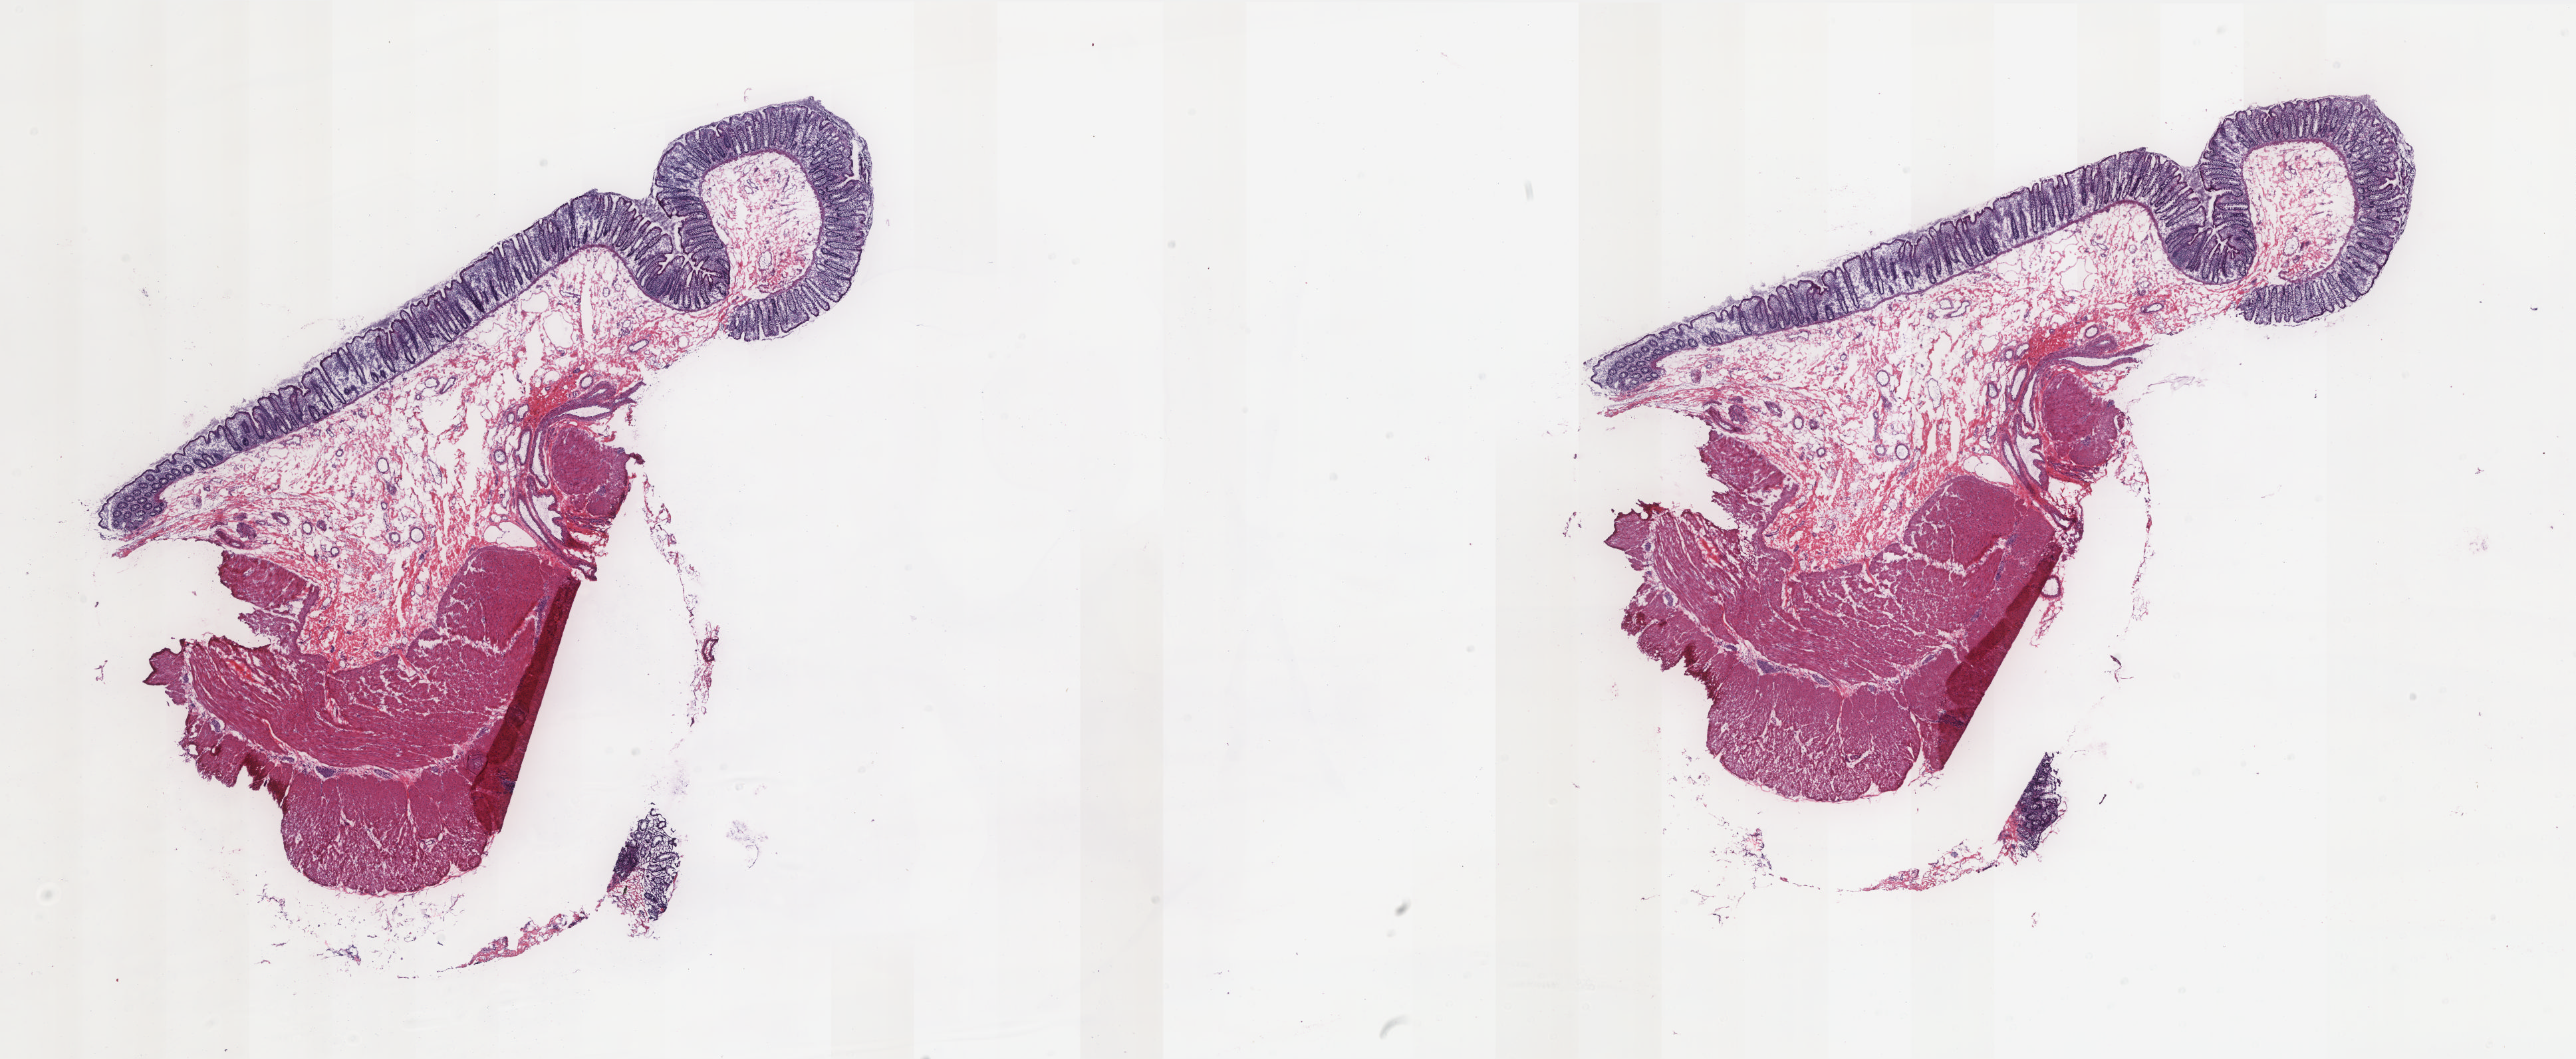
Digitized Hematoxylin and eosin (H&E) stained tissue section (whole slide), low-resolution overview of the scanned area, about 30.9 x 12.7 mm, frozen section from the bottom of the tissue portion, colon, solid tissue normal (non-tumour tissue) sample. Patient: male, age at initial diagnosis 47 years. Composition of this section per pathologist review: tumour cells 0%, normal cells 100%. Infiltration values recorded for this section: lymphocyte infiltration 35%, monocyte infiltration 10%, neutrophil infiltration 0%.
This section: solid tissue normal sample (biorepository sample class). Patient diagnosis: Mucinous adenocarcinoma (ascending colon).